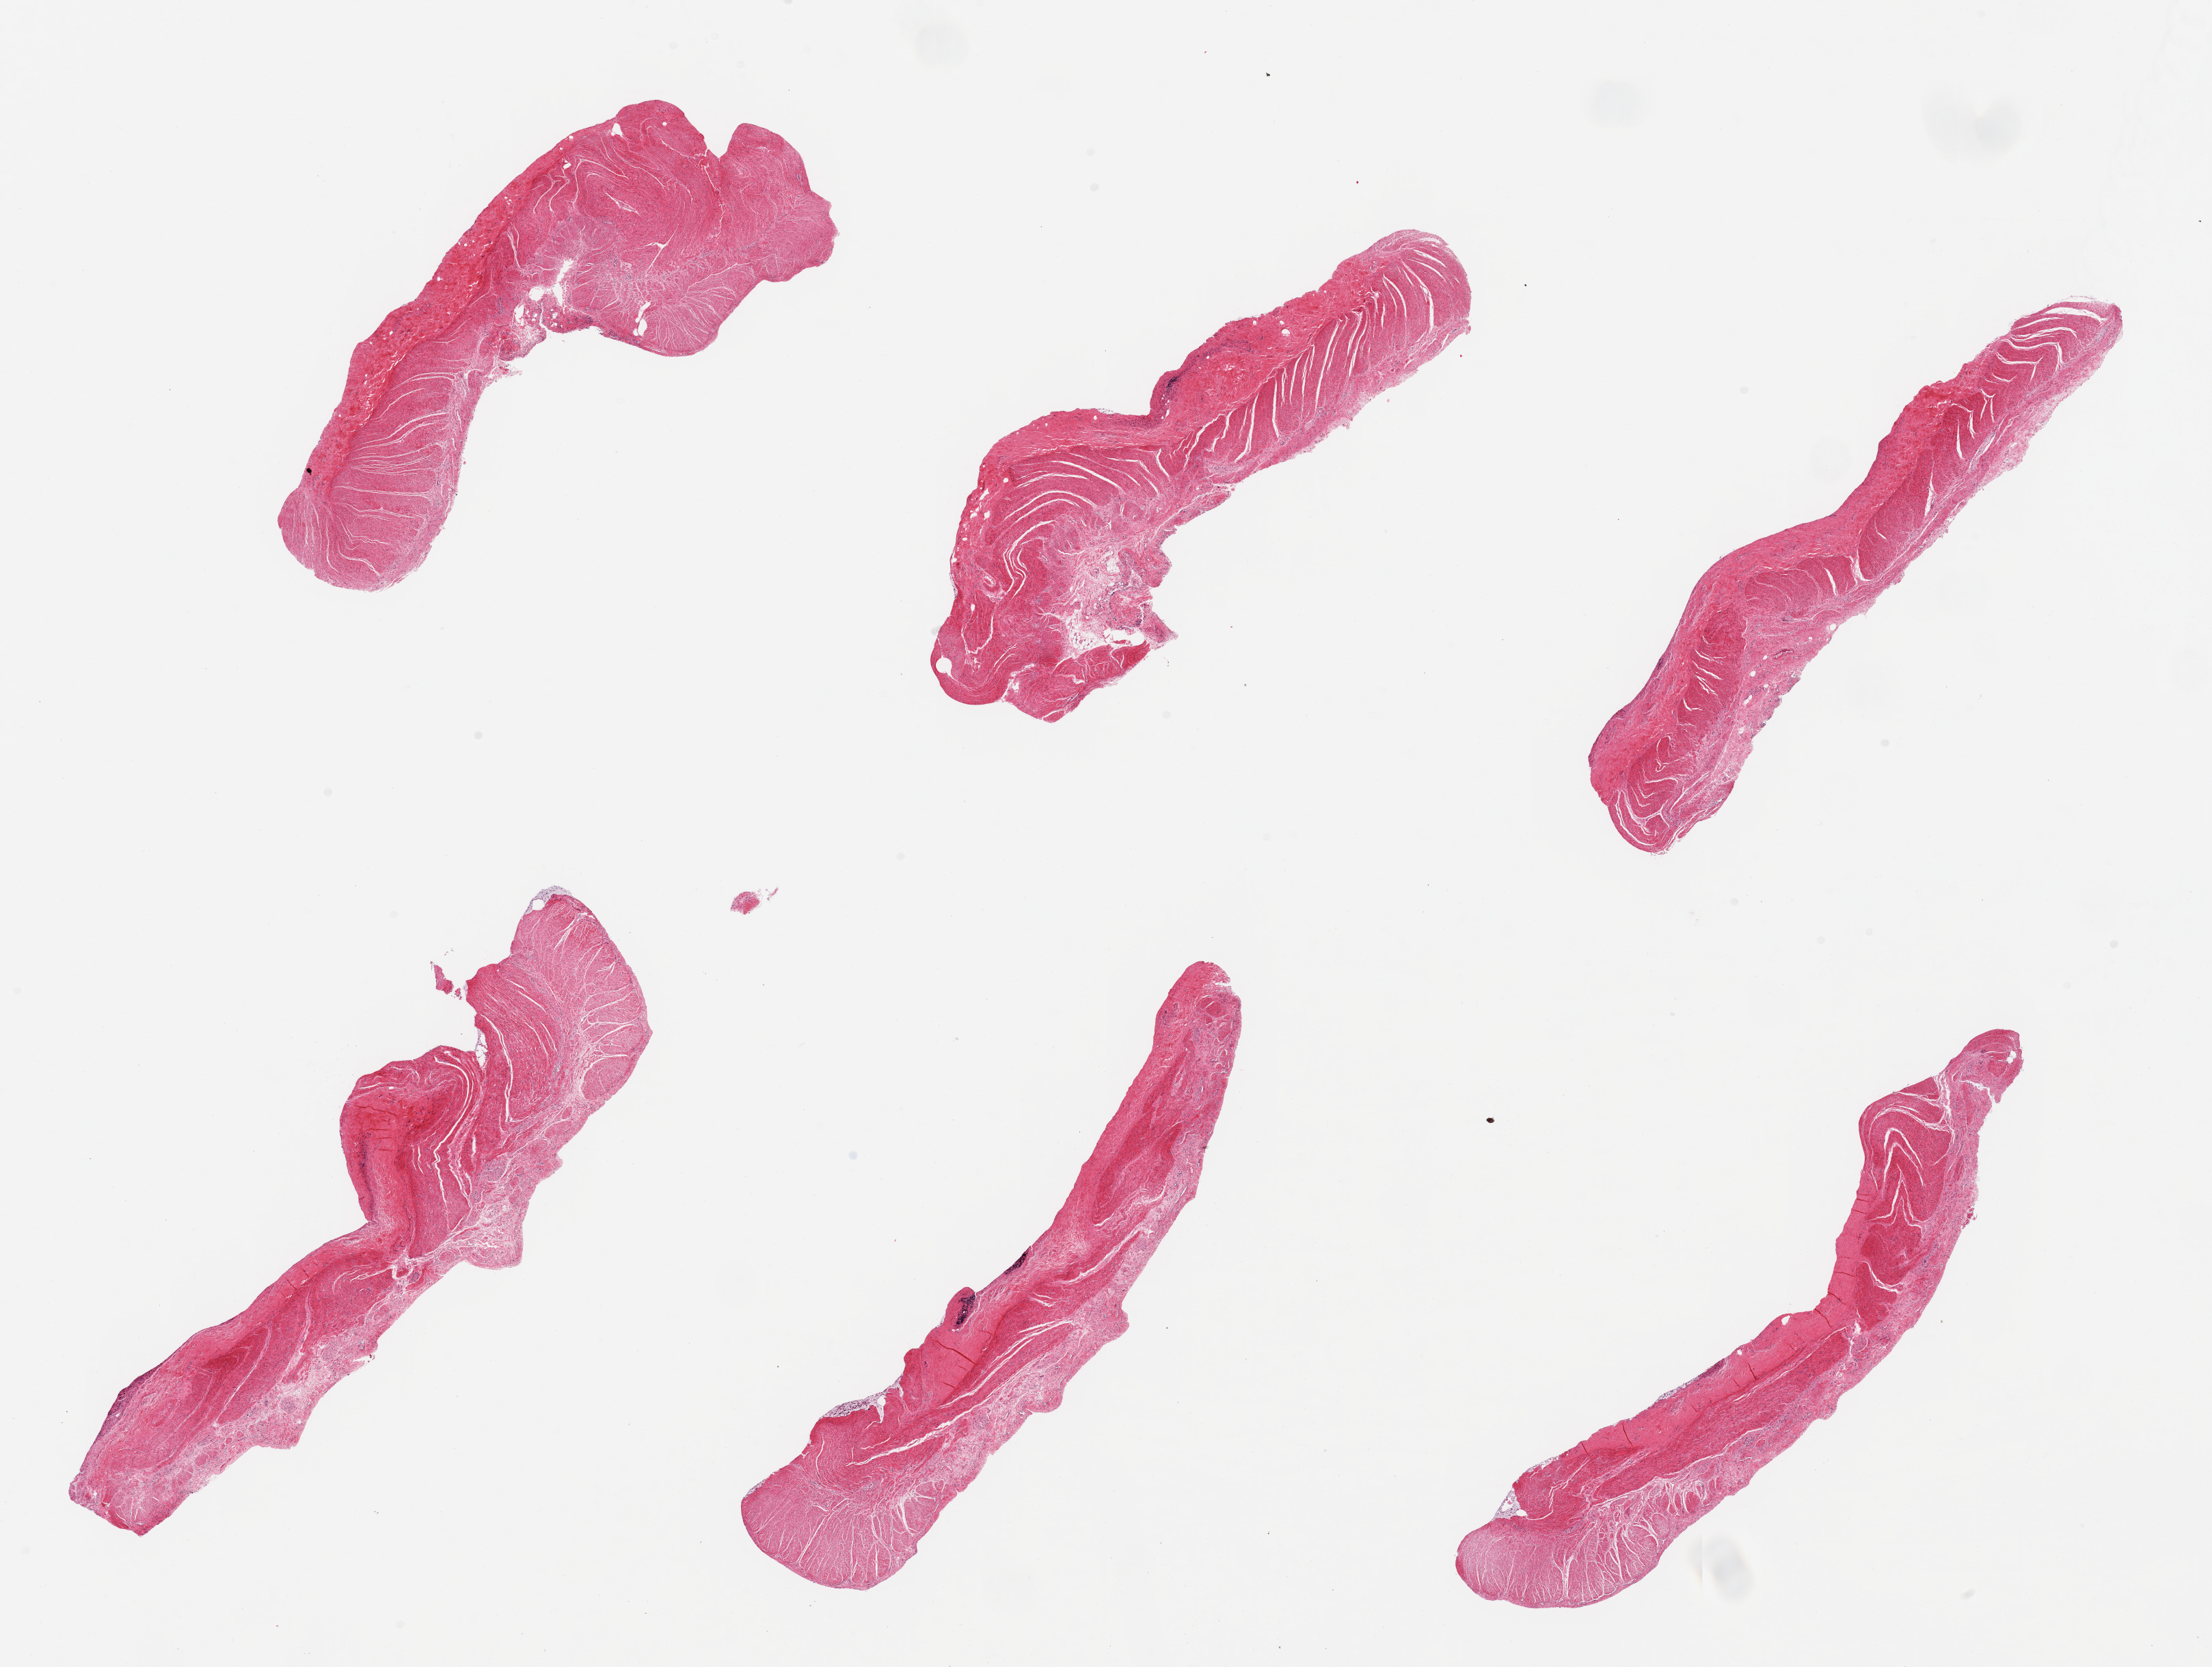
Haematoxylin and eosin whole-slide image — shown as a low-resolution overview of the whole scanned area (about 25.6 x 19.3 mm, slide scanned at 20x). PAXgene-fixed paraffin-embedded (PFPE) section. Section of sigmoid colon (target tissue). Tissue donor sample. Male donor.
• review note (as recorded): 6 pieces; up to 50% perimuscular [submucosal and subserosal] stroma